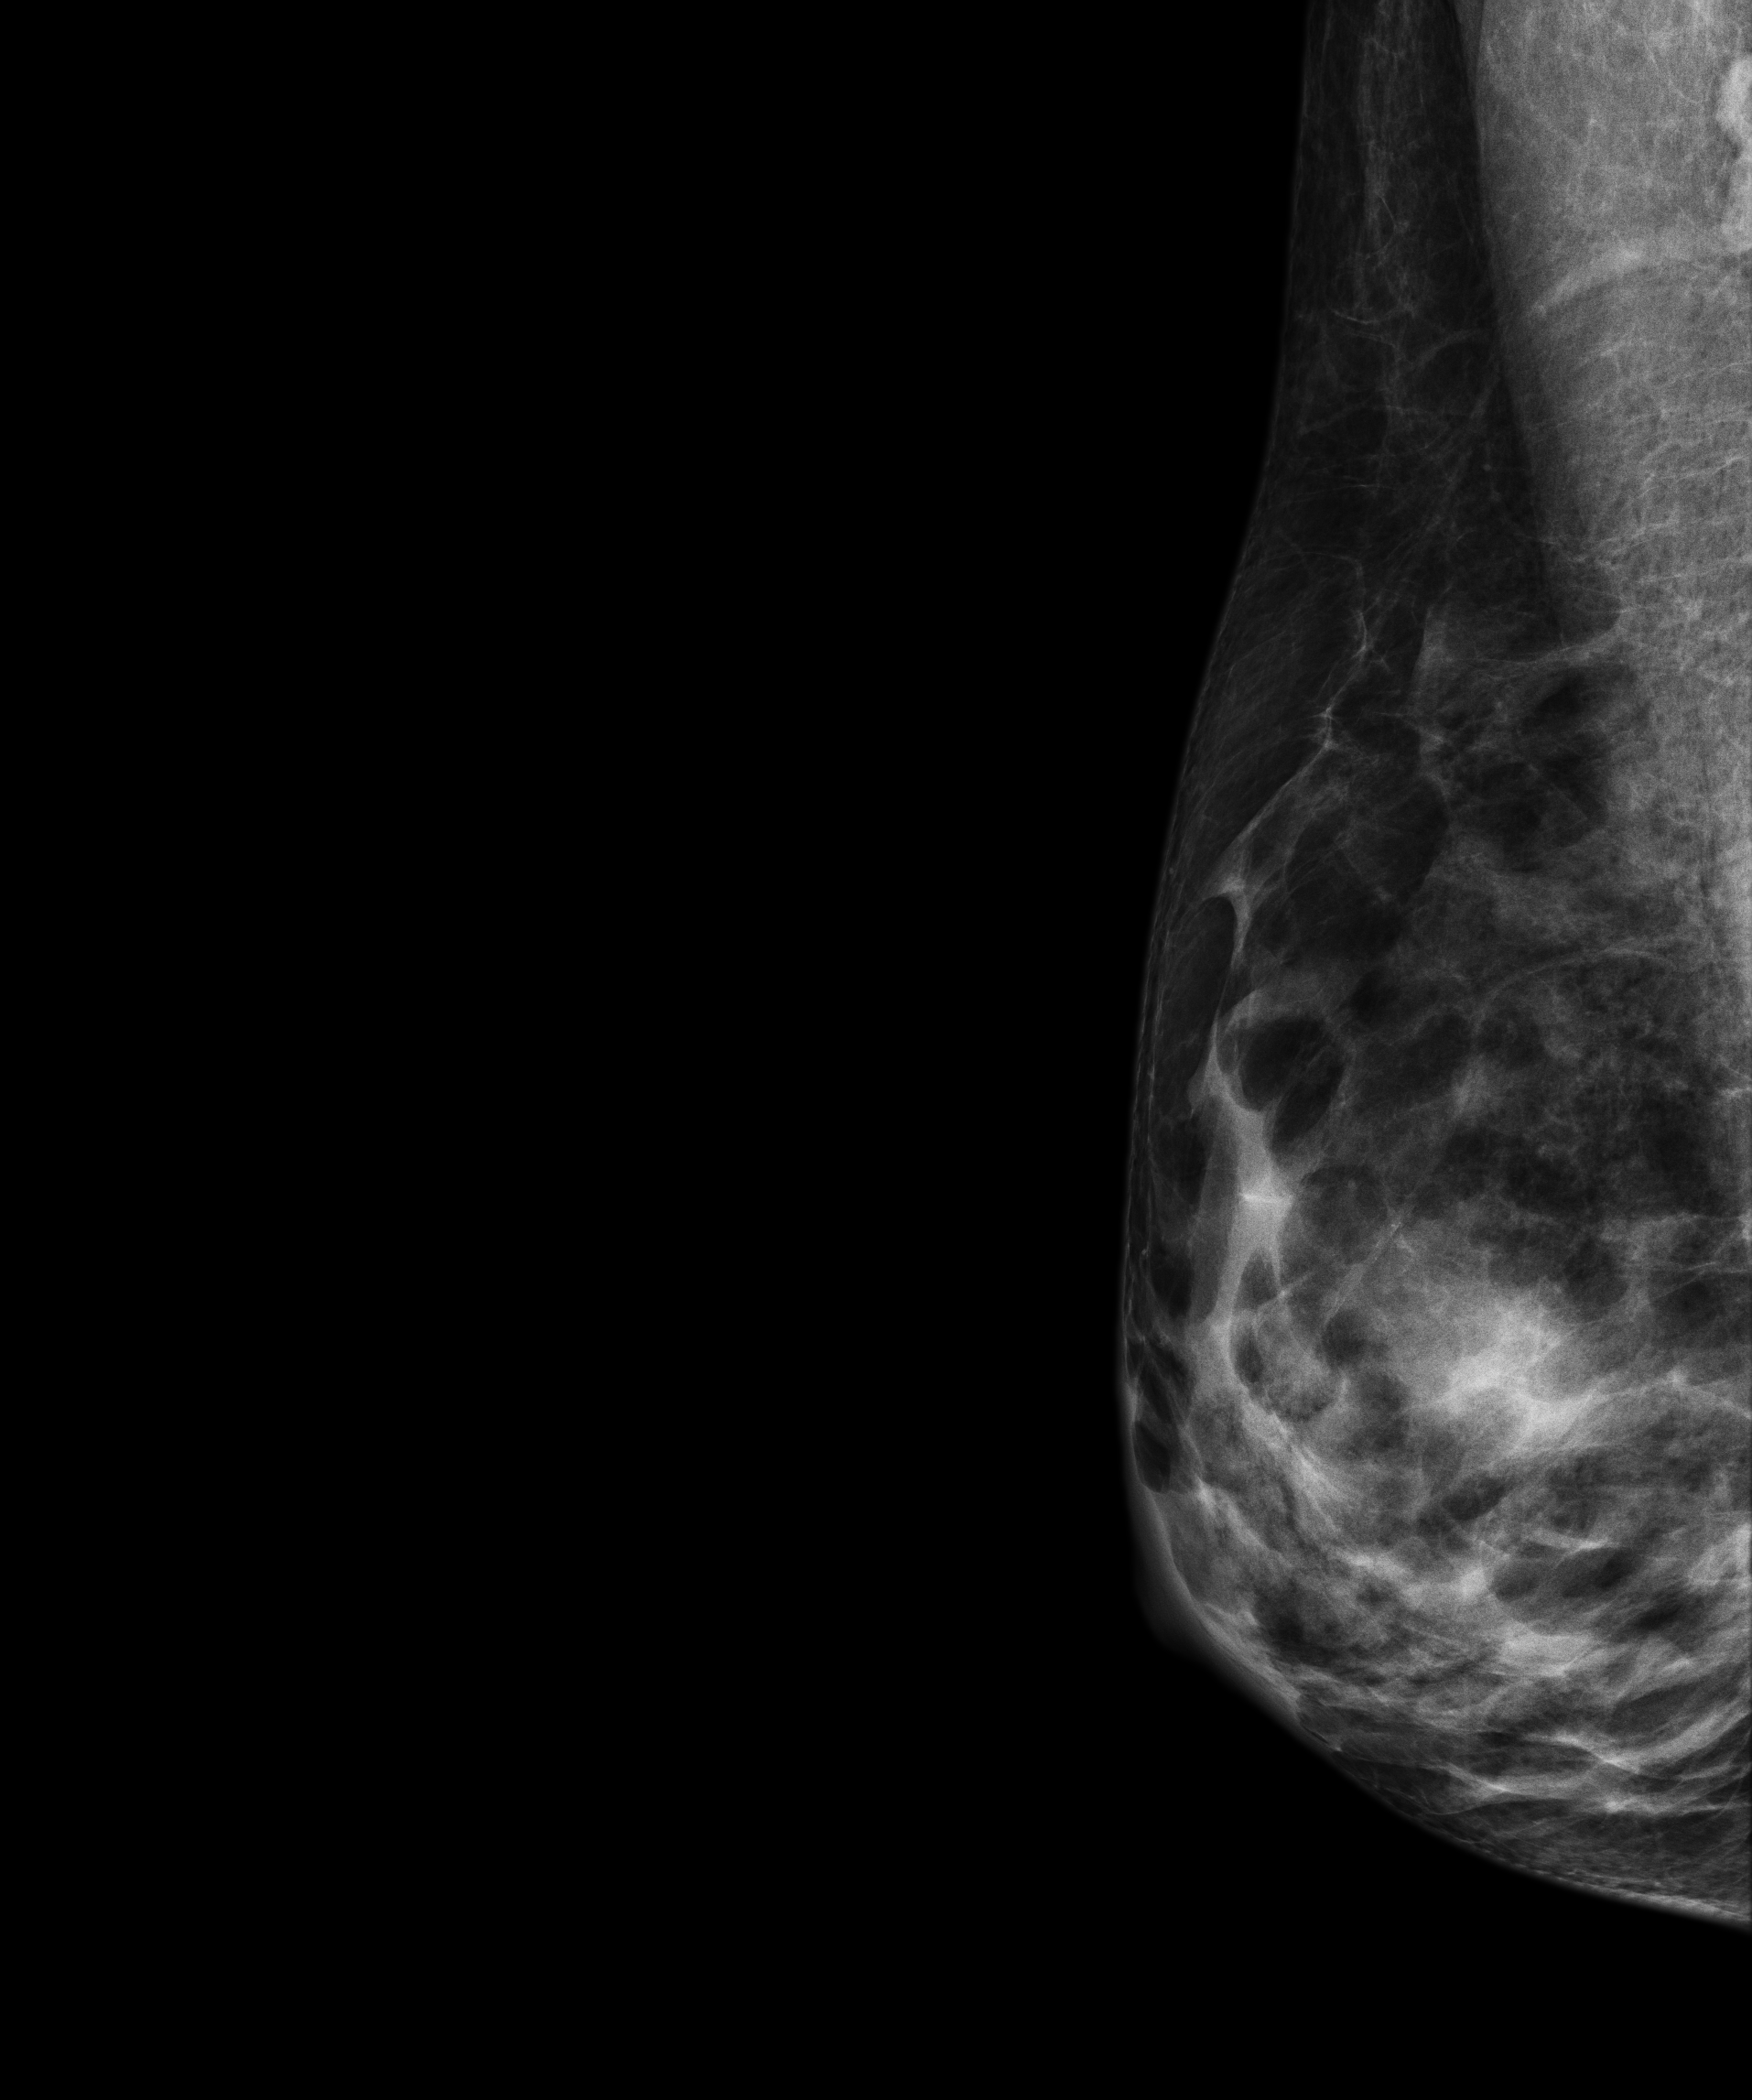
Digital mammogram (FFDM), right breast, MLO view, screening examination, compressed breast thickness 48 mm. Patient aged 66 years (female).
- BI-RADS breast density category at the screening exam (both breasts, scale 1–4): 3
- final BI-RADS category for the screening round (tomosynthesis exam, both breasts): category 1
- recall: no recall after this screen